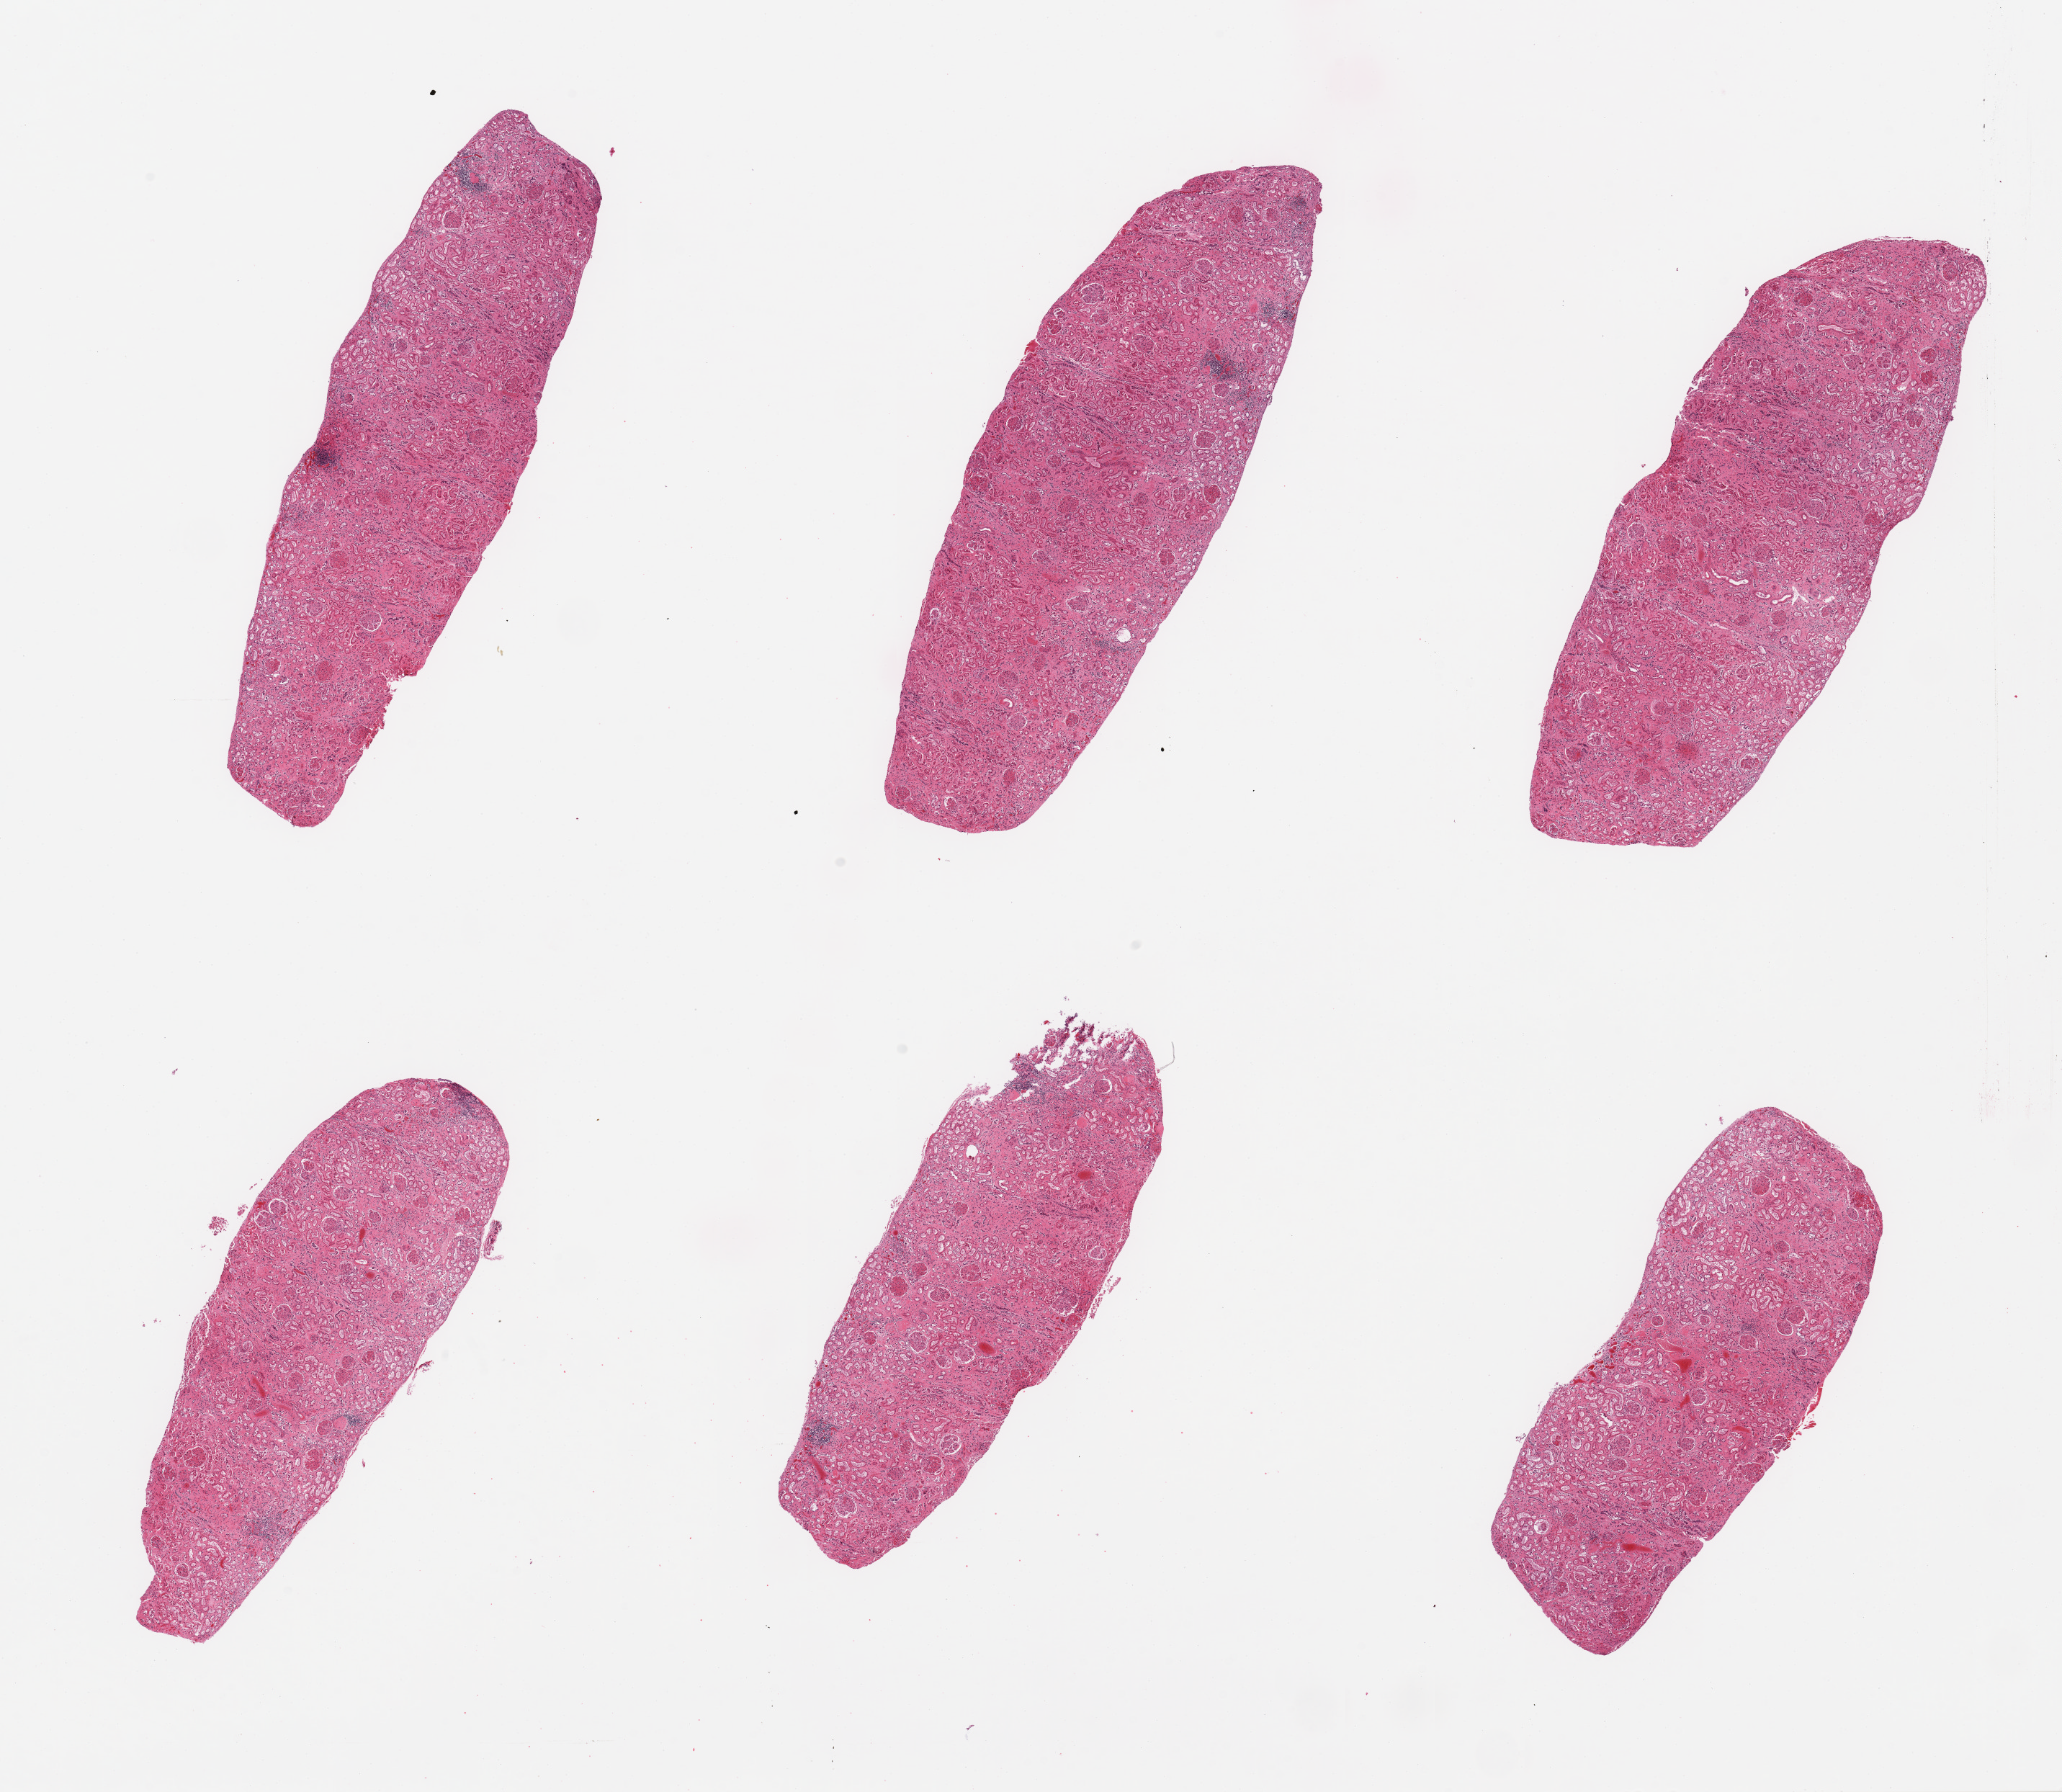
Digitized haematoxylin and eosin-stained section, a low-resolution overview of the entire scanned area, about 22.6 x 19.7 mm. PAXgene-fixed, paraffin-embedded tissue. Sampled site (target tissue): renal cortex. Donor tissue sample.
Review note (as recorded): 6 pieces; interstitial fibrosis and foci of lymphocytes consistent with chronic pyelonephritis; tubules are severely autolyzed, glomeruli better preserved.